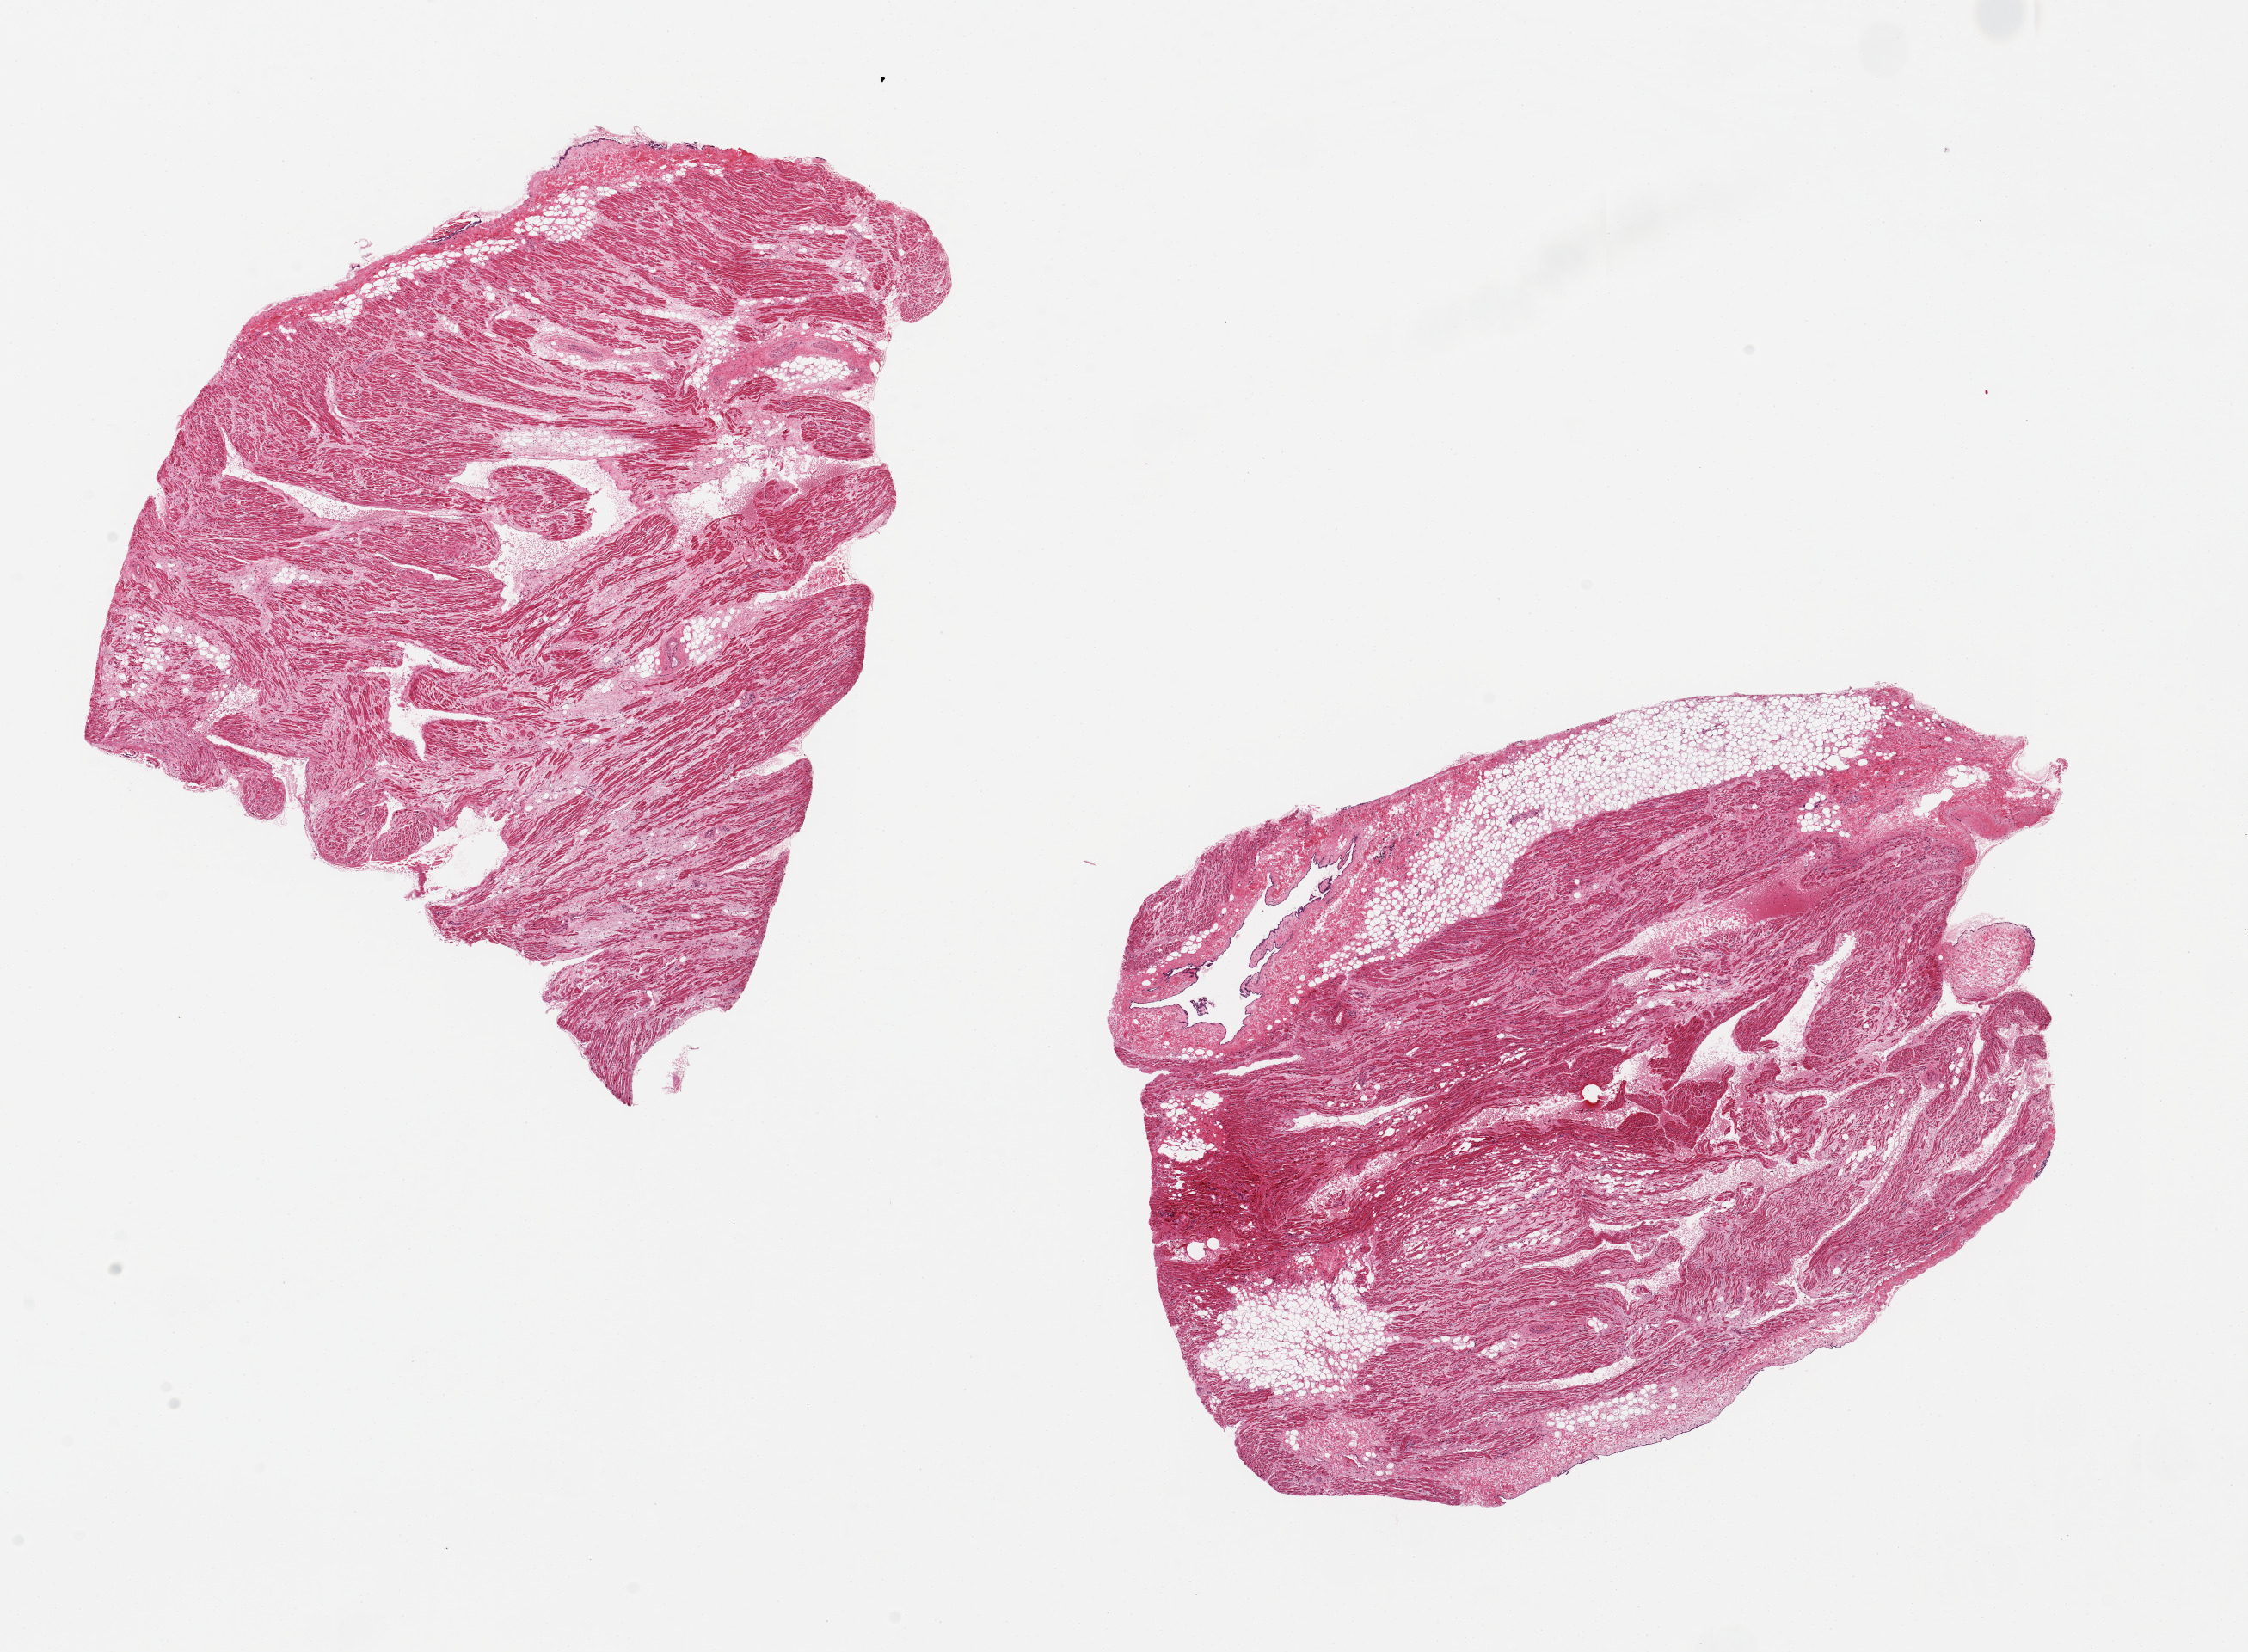
Whole-slide image, H&E stain, brightfield, whole scanned area (about 20.7 x 15.2 mm, slide scanned at 20x) shown as a low-resolution overview. PAXgene-fixed, paraffin-embedded tissue. Section of auricular appendage (target tissue). Tissue donor sample. Donor: male.
Reviewer comment on this tissue sample: 2 pieces. 8x7 & 9x7mm.